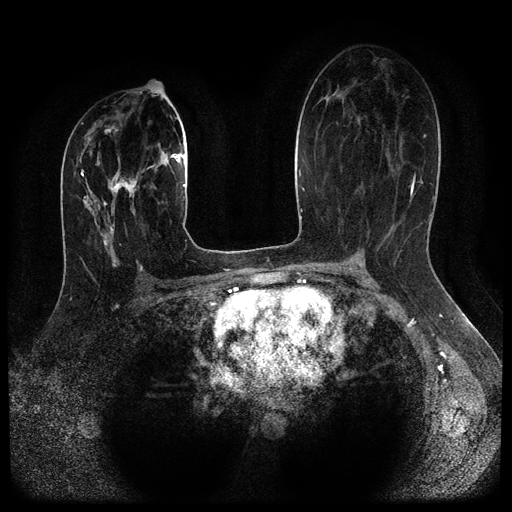
Breast MRI (dynamic contrast-enhanced, multi-phase), one axial slice; position 57 of 116 along the scan axis; dynamic contrast-enhanced series, time point 2 of 5 at this slice position (early post-contrast); 1.5 T; TE 2.6 ms, TR 5.4 ms; 2 mm slice thickness; 512 × 512 image matrix. Patient: female, 29 years.
Outlined on this slice (semi-automatic segmentation, software-assisted and operator-edited):
- breast lesion (labelled 'tumour' in the annotation; benign lesions carry a separate 'benign' label): bounding box (x1, y1, x2, y2) in pixels: (108, 171, 145, 199)